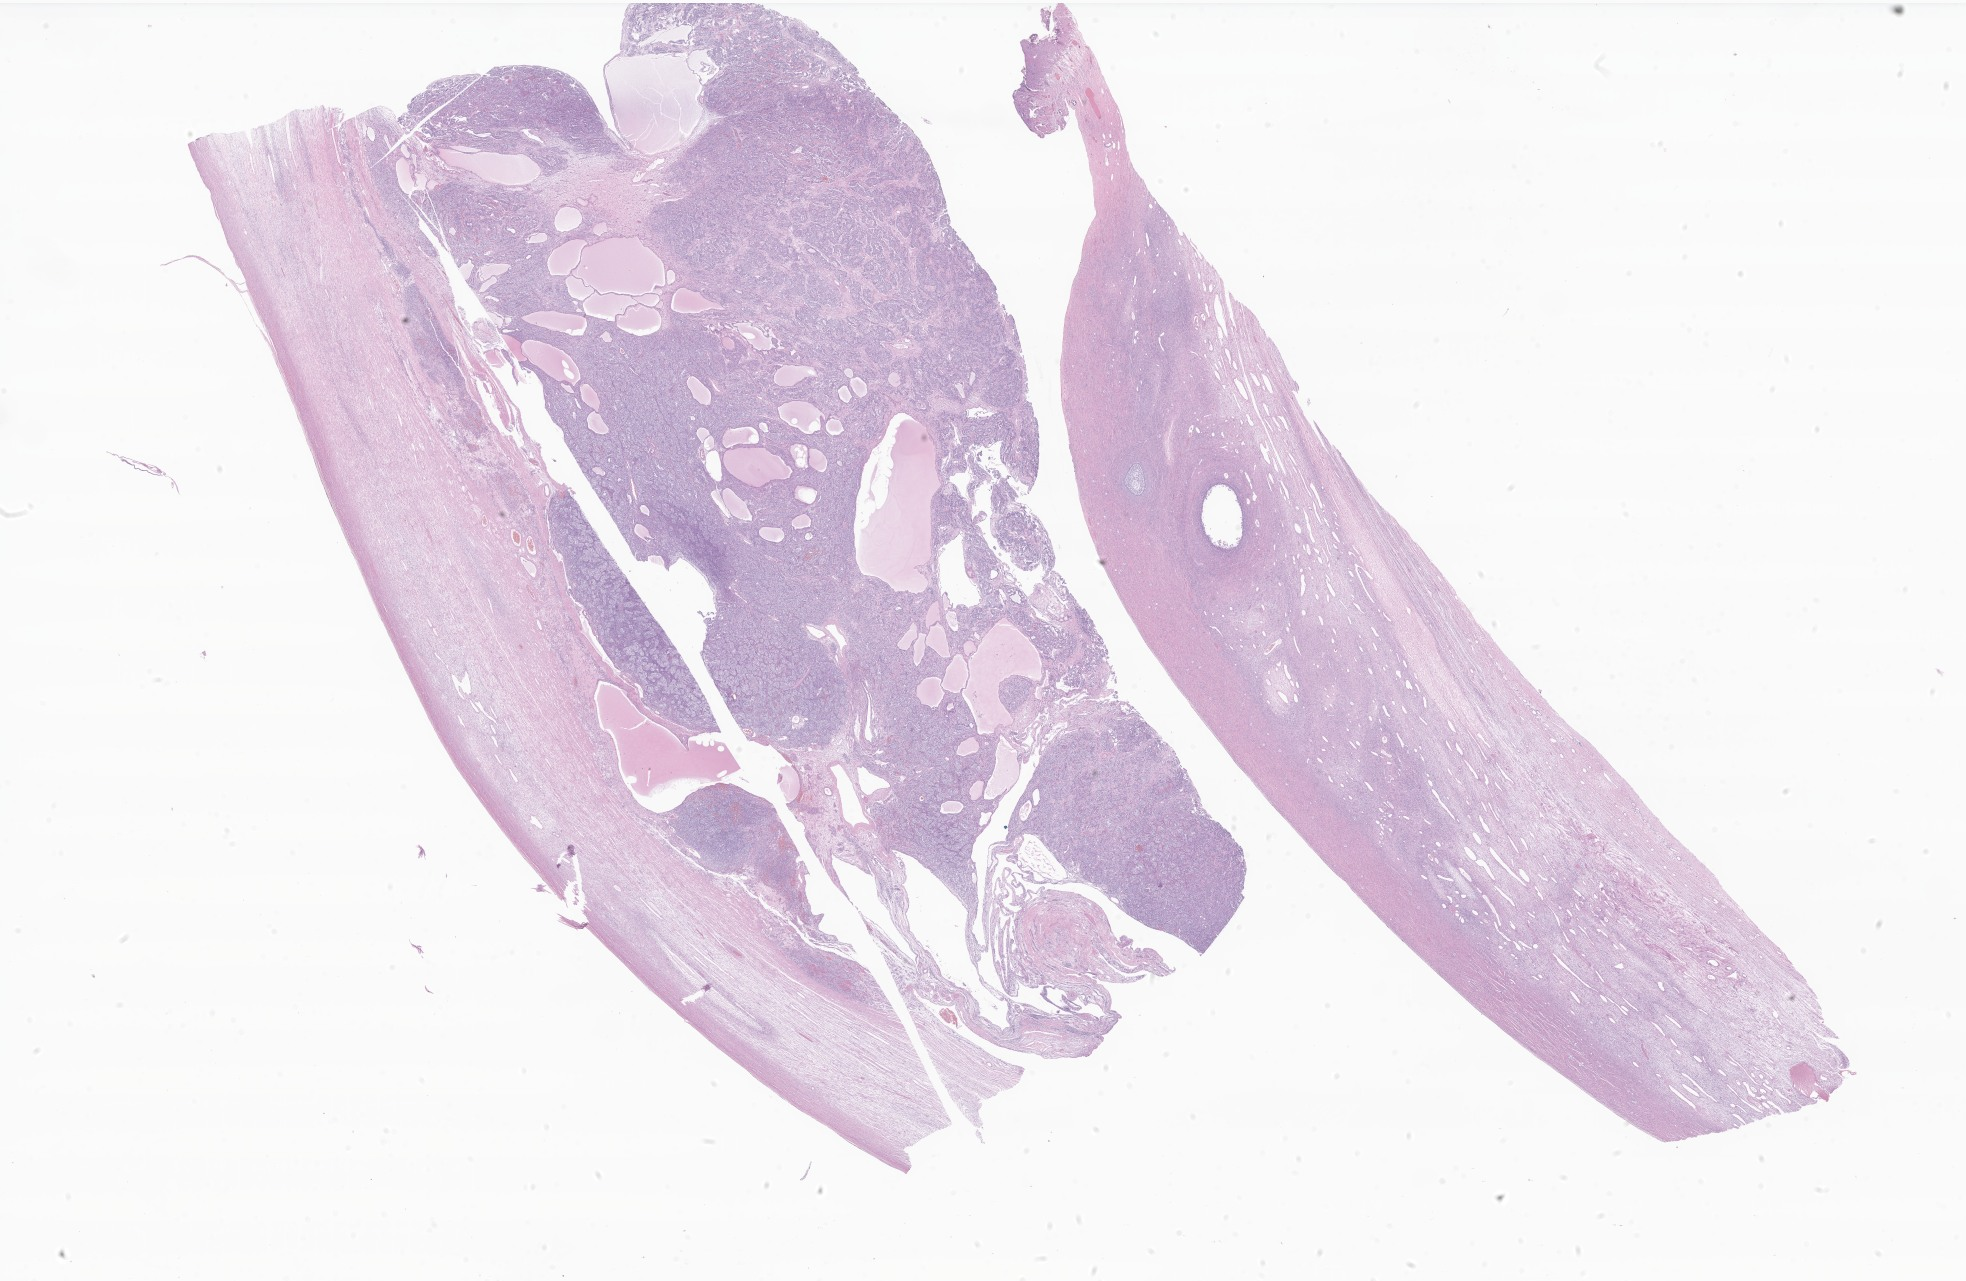
Haematoxylin and eosin whole-slide image of tumor tissue from the ovary — low-resolution overview of the scanned area, about 33.2 x 21.6 mm. Formalin-fixed paraffin-embedded section. Female patient, age 198 months (16 years 6 months).
Diagnosis (ICD-O-3 morphology term): Sertoli-Leydig cell tumor of intermediate differentiation, NOS.